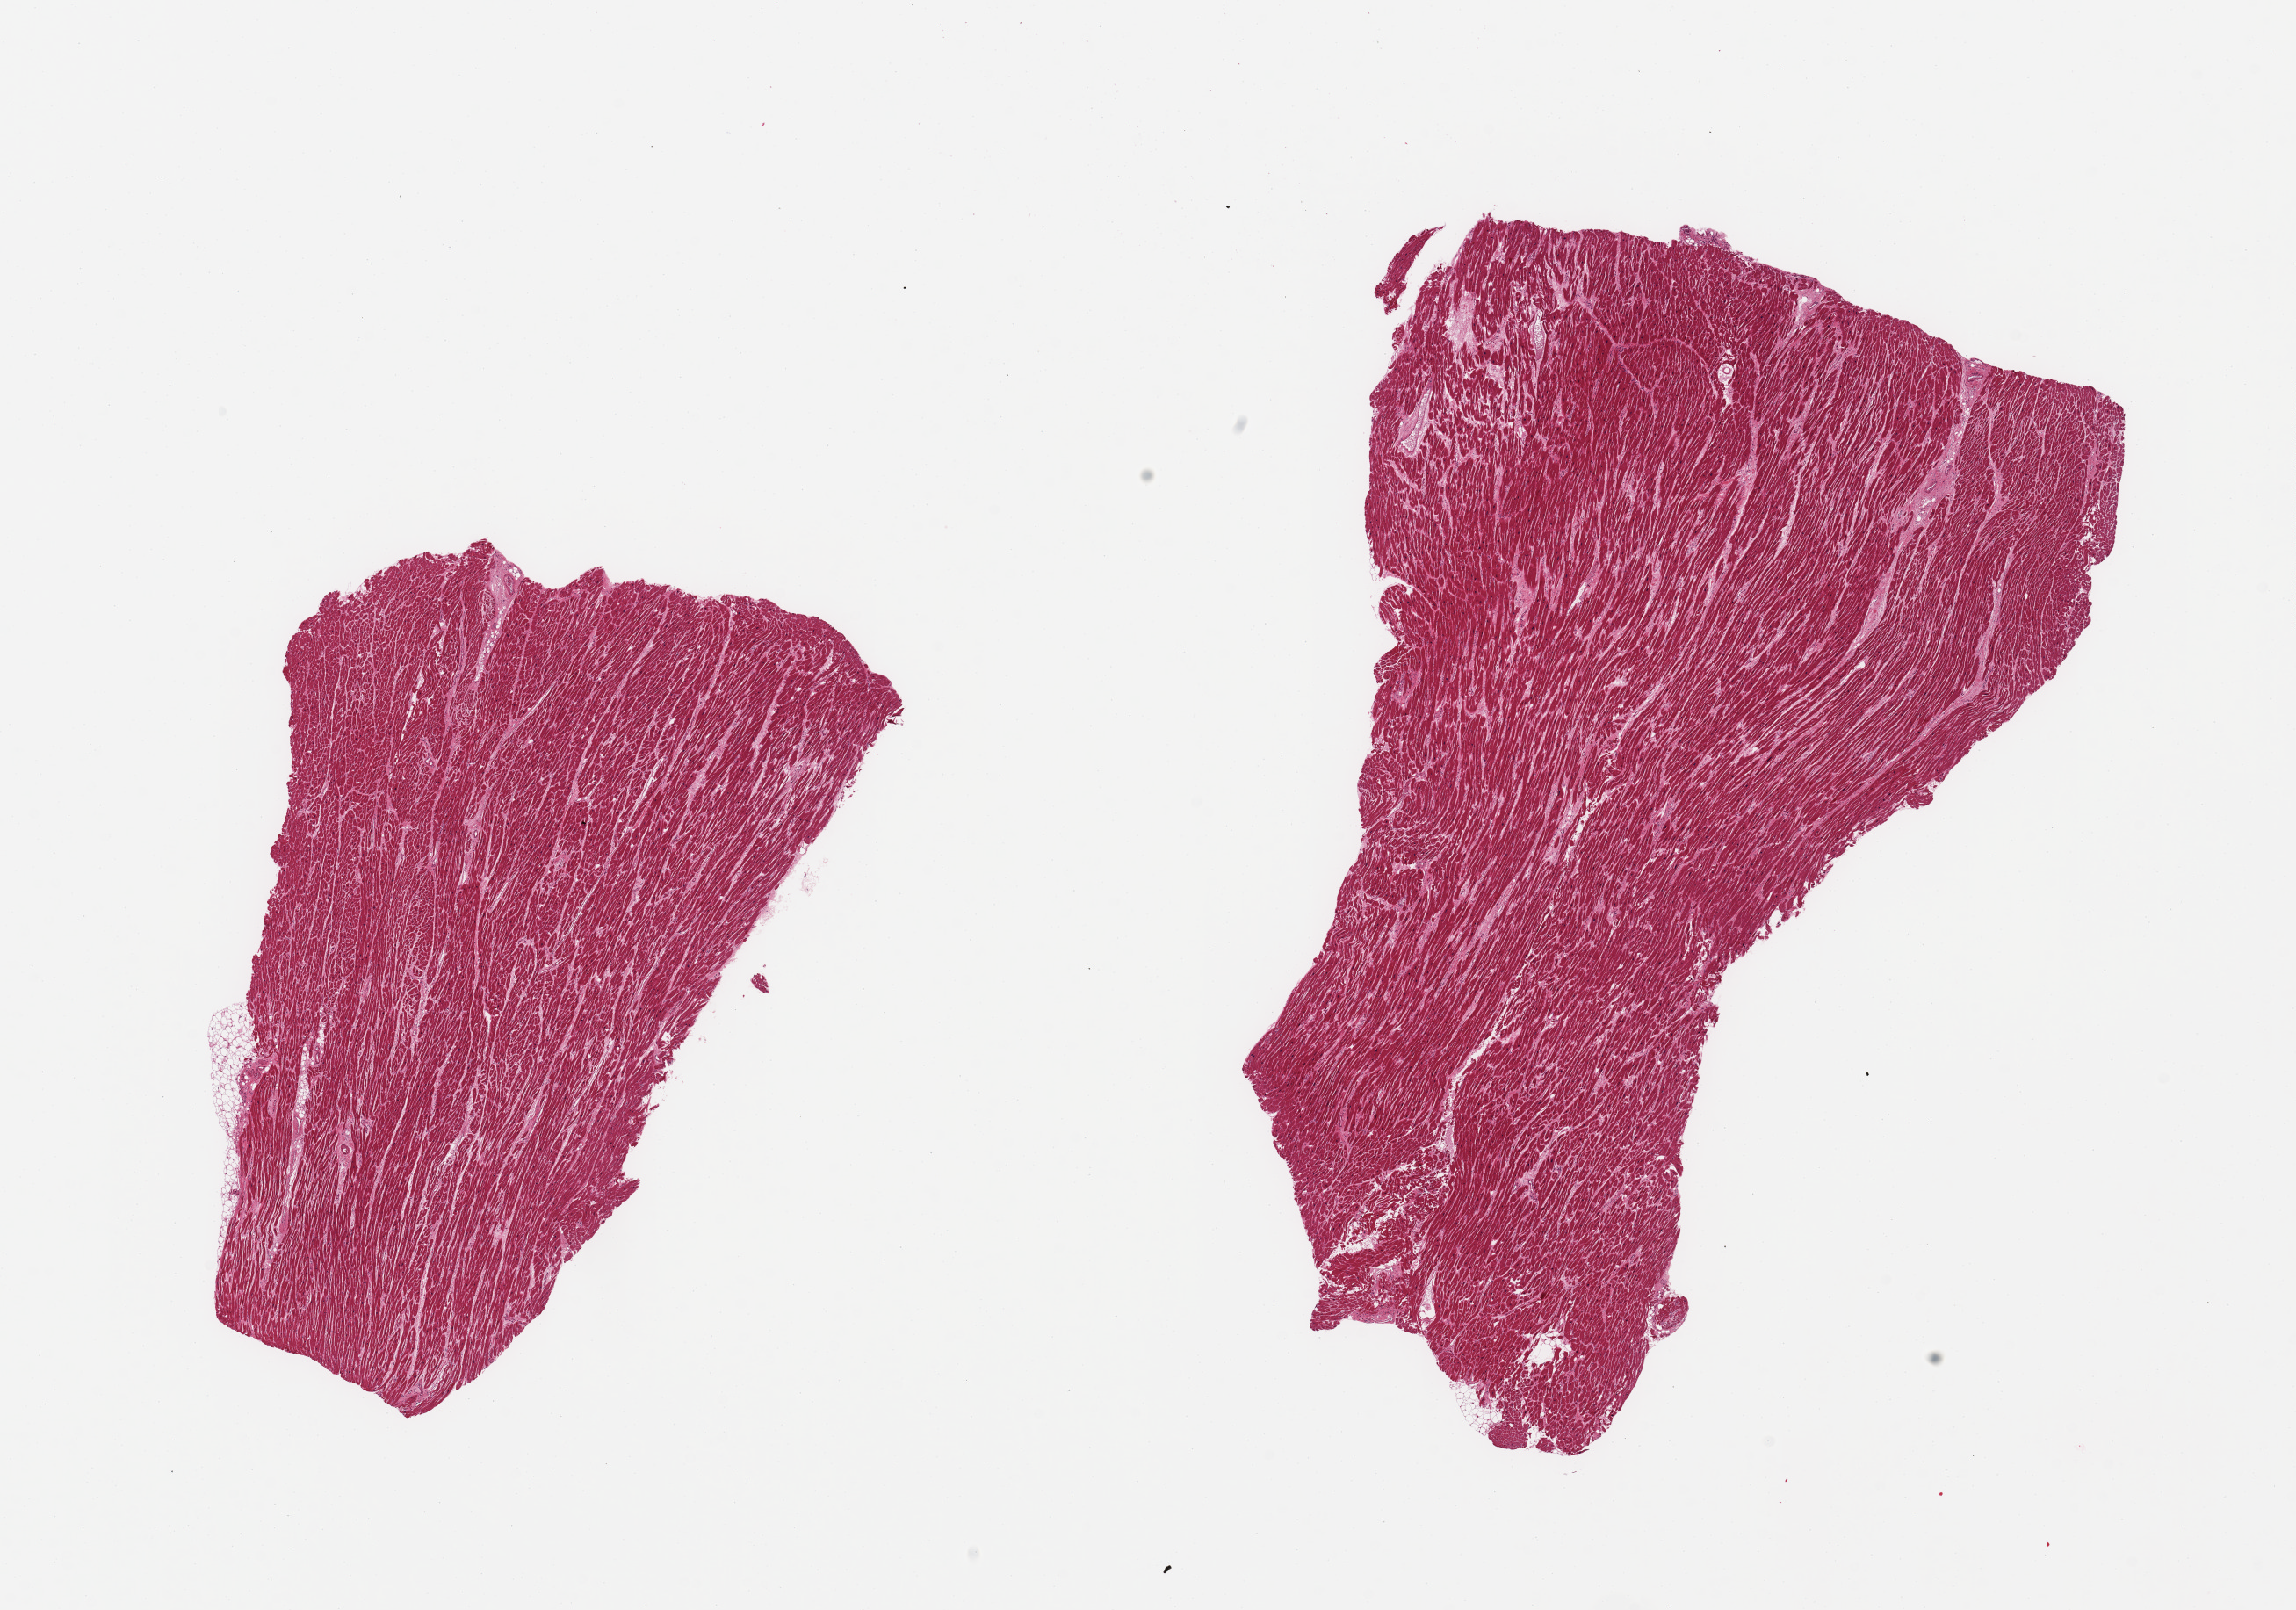
Hematoxylin and eosin (H&E) whole-slide image — a low-resolution overview of the entire scanned area, about 20.7 x 14.5 mm (acquisition: 20x scan). PAXgene-fixed paraffin-embedded (PFPE) section. Sampled site (target tissue): heart. Donor tissue sample.
Review note (as recorded): 2 pieces; mild focal increase in fibrous tissue.